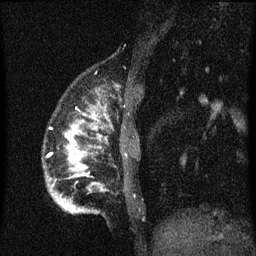
Breast MRI (dynamic contrast-enhanced), one sagittal slice. Slice 13 of 60 in the series (ordered by position). Dynamic contrast-enhanced series, image 2 of 3 at this slice position (ordered by acquisition). 1.5 T. TE 4.2 ms, TR 8.4 ms. 2 mm slice thickness. 256 × 256 image matrix, field of view 180 × 180 mm. Patient: female, 34 years. From the clinical record (not read from this slice): setting: breast cancer imaged before/during neoadjuvant chemotherapy; receptor status: HR-positive, HER2-negative.
Annotated regions visible in this slice (semi-automatic segmentation, software-assisted and operator-edited):
- analysis volume of interest (the breast-tissue region the enhancement analysis was run in; not a lesion): bounding box [x1, y1, x2, y2] px = [44, 92, 141, 215]
- tumour enhancement mask (voxels above the 70 % enhancement threshold inside the analysis volume of interest): [66, 114, 97, 177]